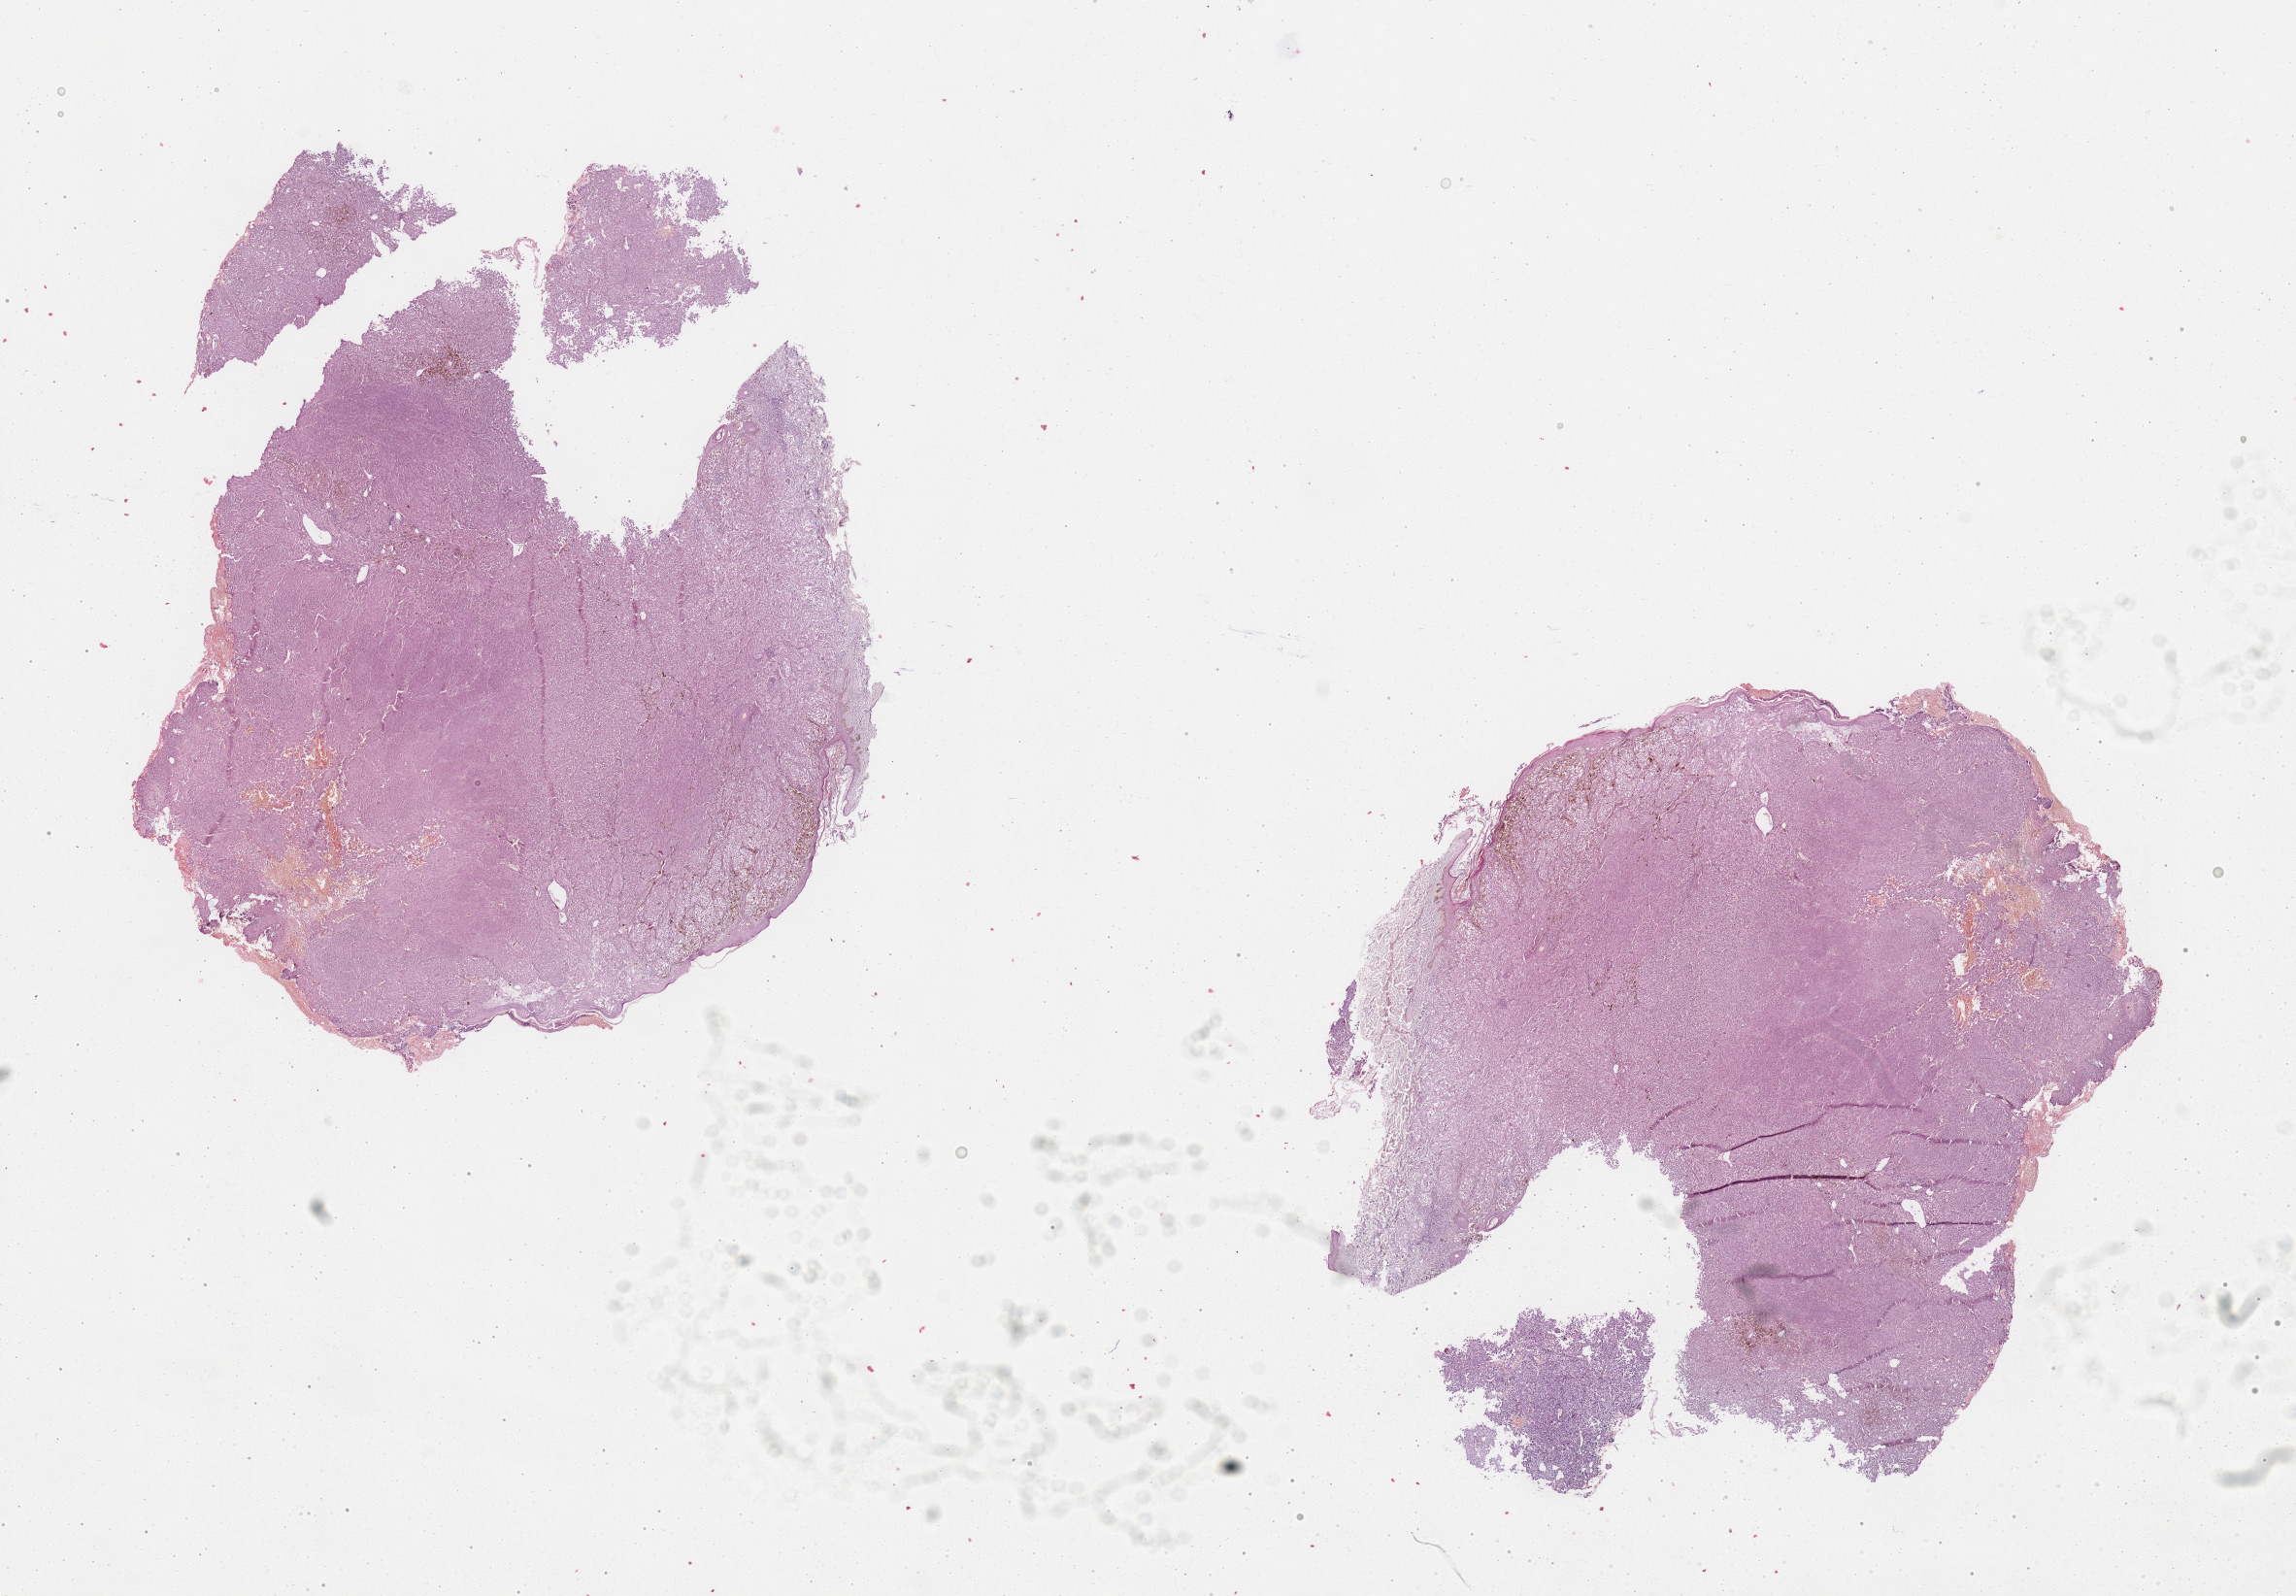
H&E-stained whole-slide image, low-resolution overview of the scanned area, about 18.7 x 13.0 mm. Tumour tissue sample, sampled site: trunk. Patient: female, age 86 years. Slide review estimates, as recorded: tumour nuclei 95%, necrosis 0%.
* histologic diagnosis: Malignant melanoma, NOS
* primary tumour site (as recorded): trunk
* AJCC pathologic stage: IIC